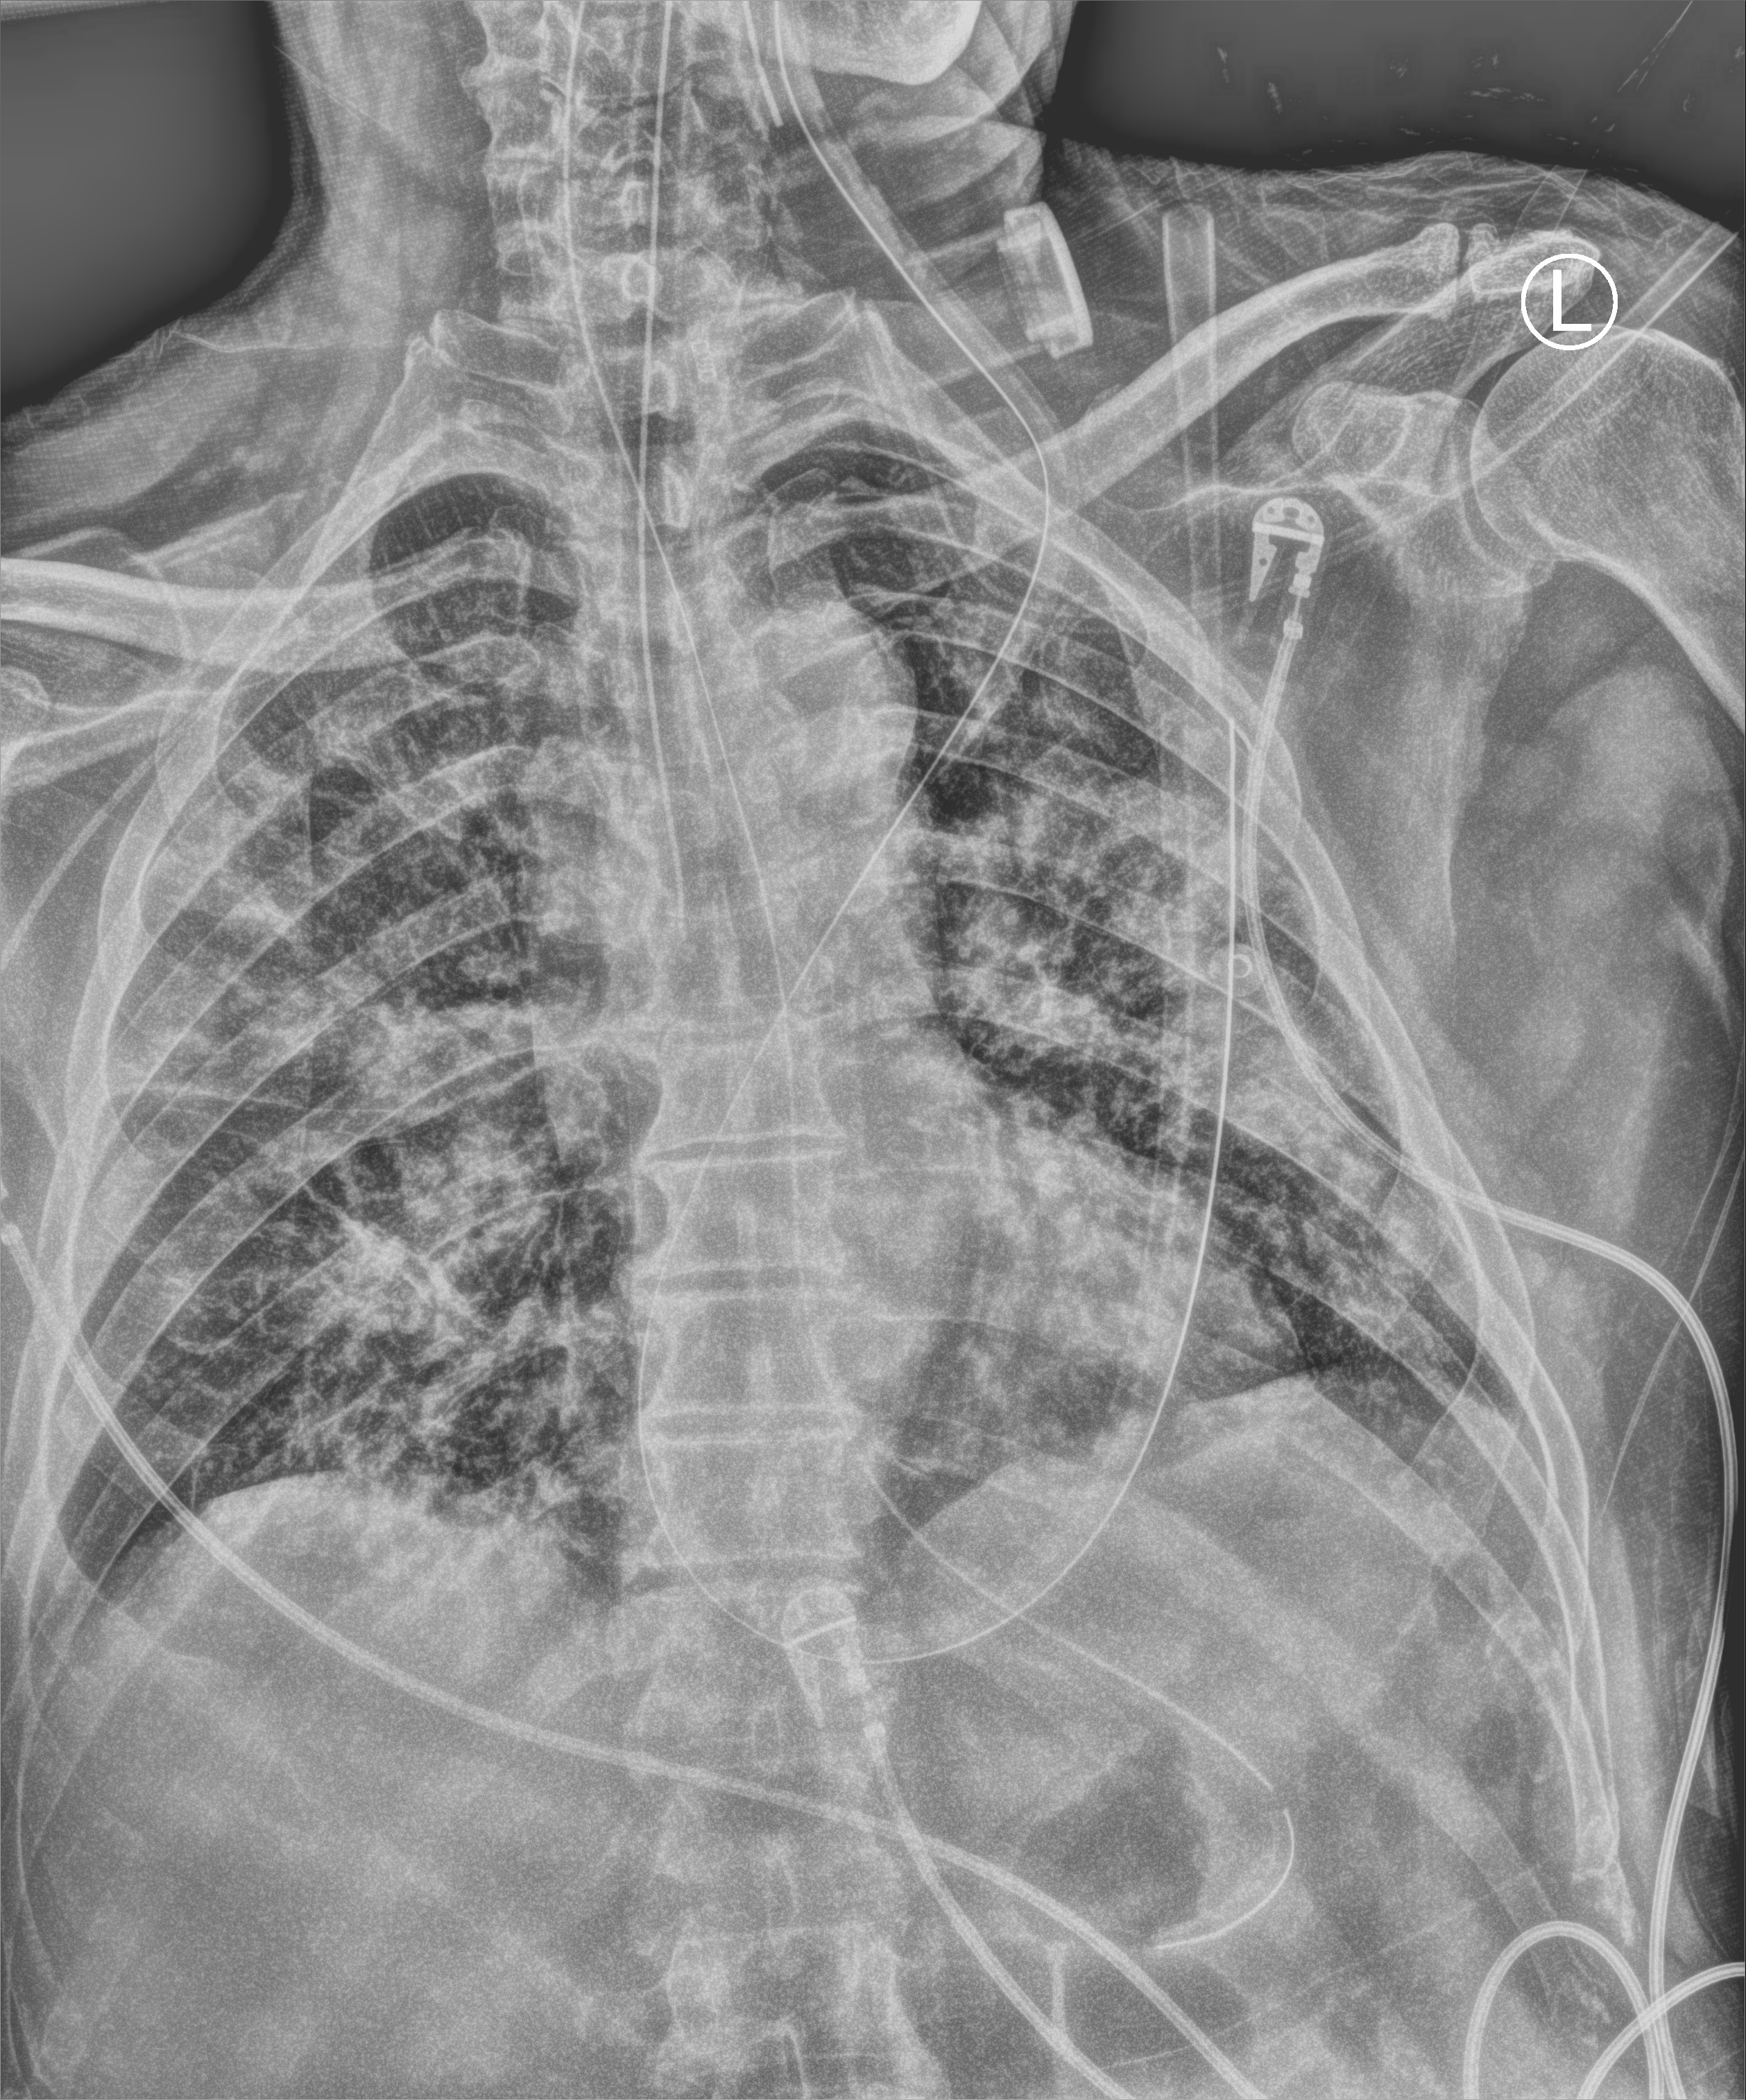
Bedside chest radiograph (computed radiography). Patient hospitalised with COVID-19; male, aged 60–74 years.
Hospital-stay facts (about this admission, not read from this image; timing relative to this image not recorded): admitted to intensive care during this hospital stay: yes; mechanically ventilated during this hospital stay: yes; length of hospital stay: 20 days.